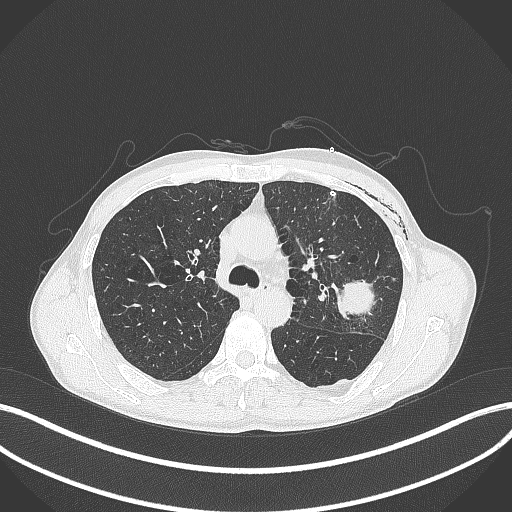
Chest CT, one axial slice. Lung window (W 1500 / L -600 HU). 1 mm slice thickness. 512 × 512 image matrix, field of view 400 × 400 mm. Patient: male, 58 years. Case-level facts recorded for this patient, not image findings: clinical TNM (as recorded): T3 N0 M0.
Annotated regions visible in this slice (bounding box drawn by a radiologist):
- lung tumour (recorded histology: adenocarcinoma): bounding box <336,278,376,319> (left, top, right, bottom; pixels)